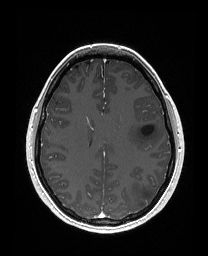
Brain MRI from a brain-tumour surgery series, one axial slice. Position 104 of 176 along the scan axis. T1-weighted post-contrast. 1 mm slice thickness. 208 × 256 image matrix. Case-level facts recorded for this patient, not image findings: histopathology: Astrocytoma; WHO grade: 3; IDH mutation: yes; tumour location: Left Frontal.
Annotated regions visible in this slice (expert manual segmentation):
- tumour: bounding box [x1, y1, x2, y2] px = [126, 121, 160, 150]